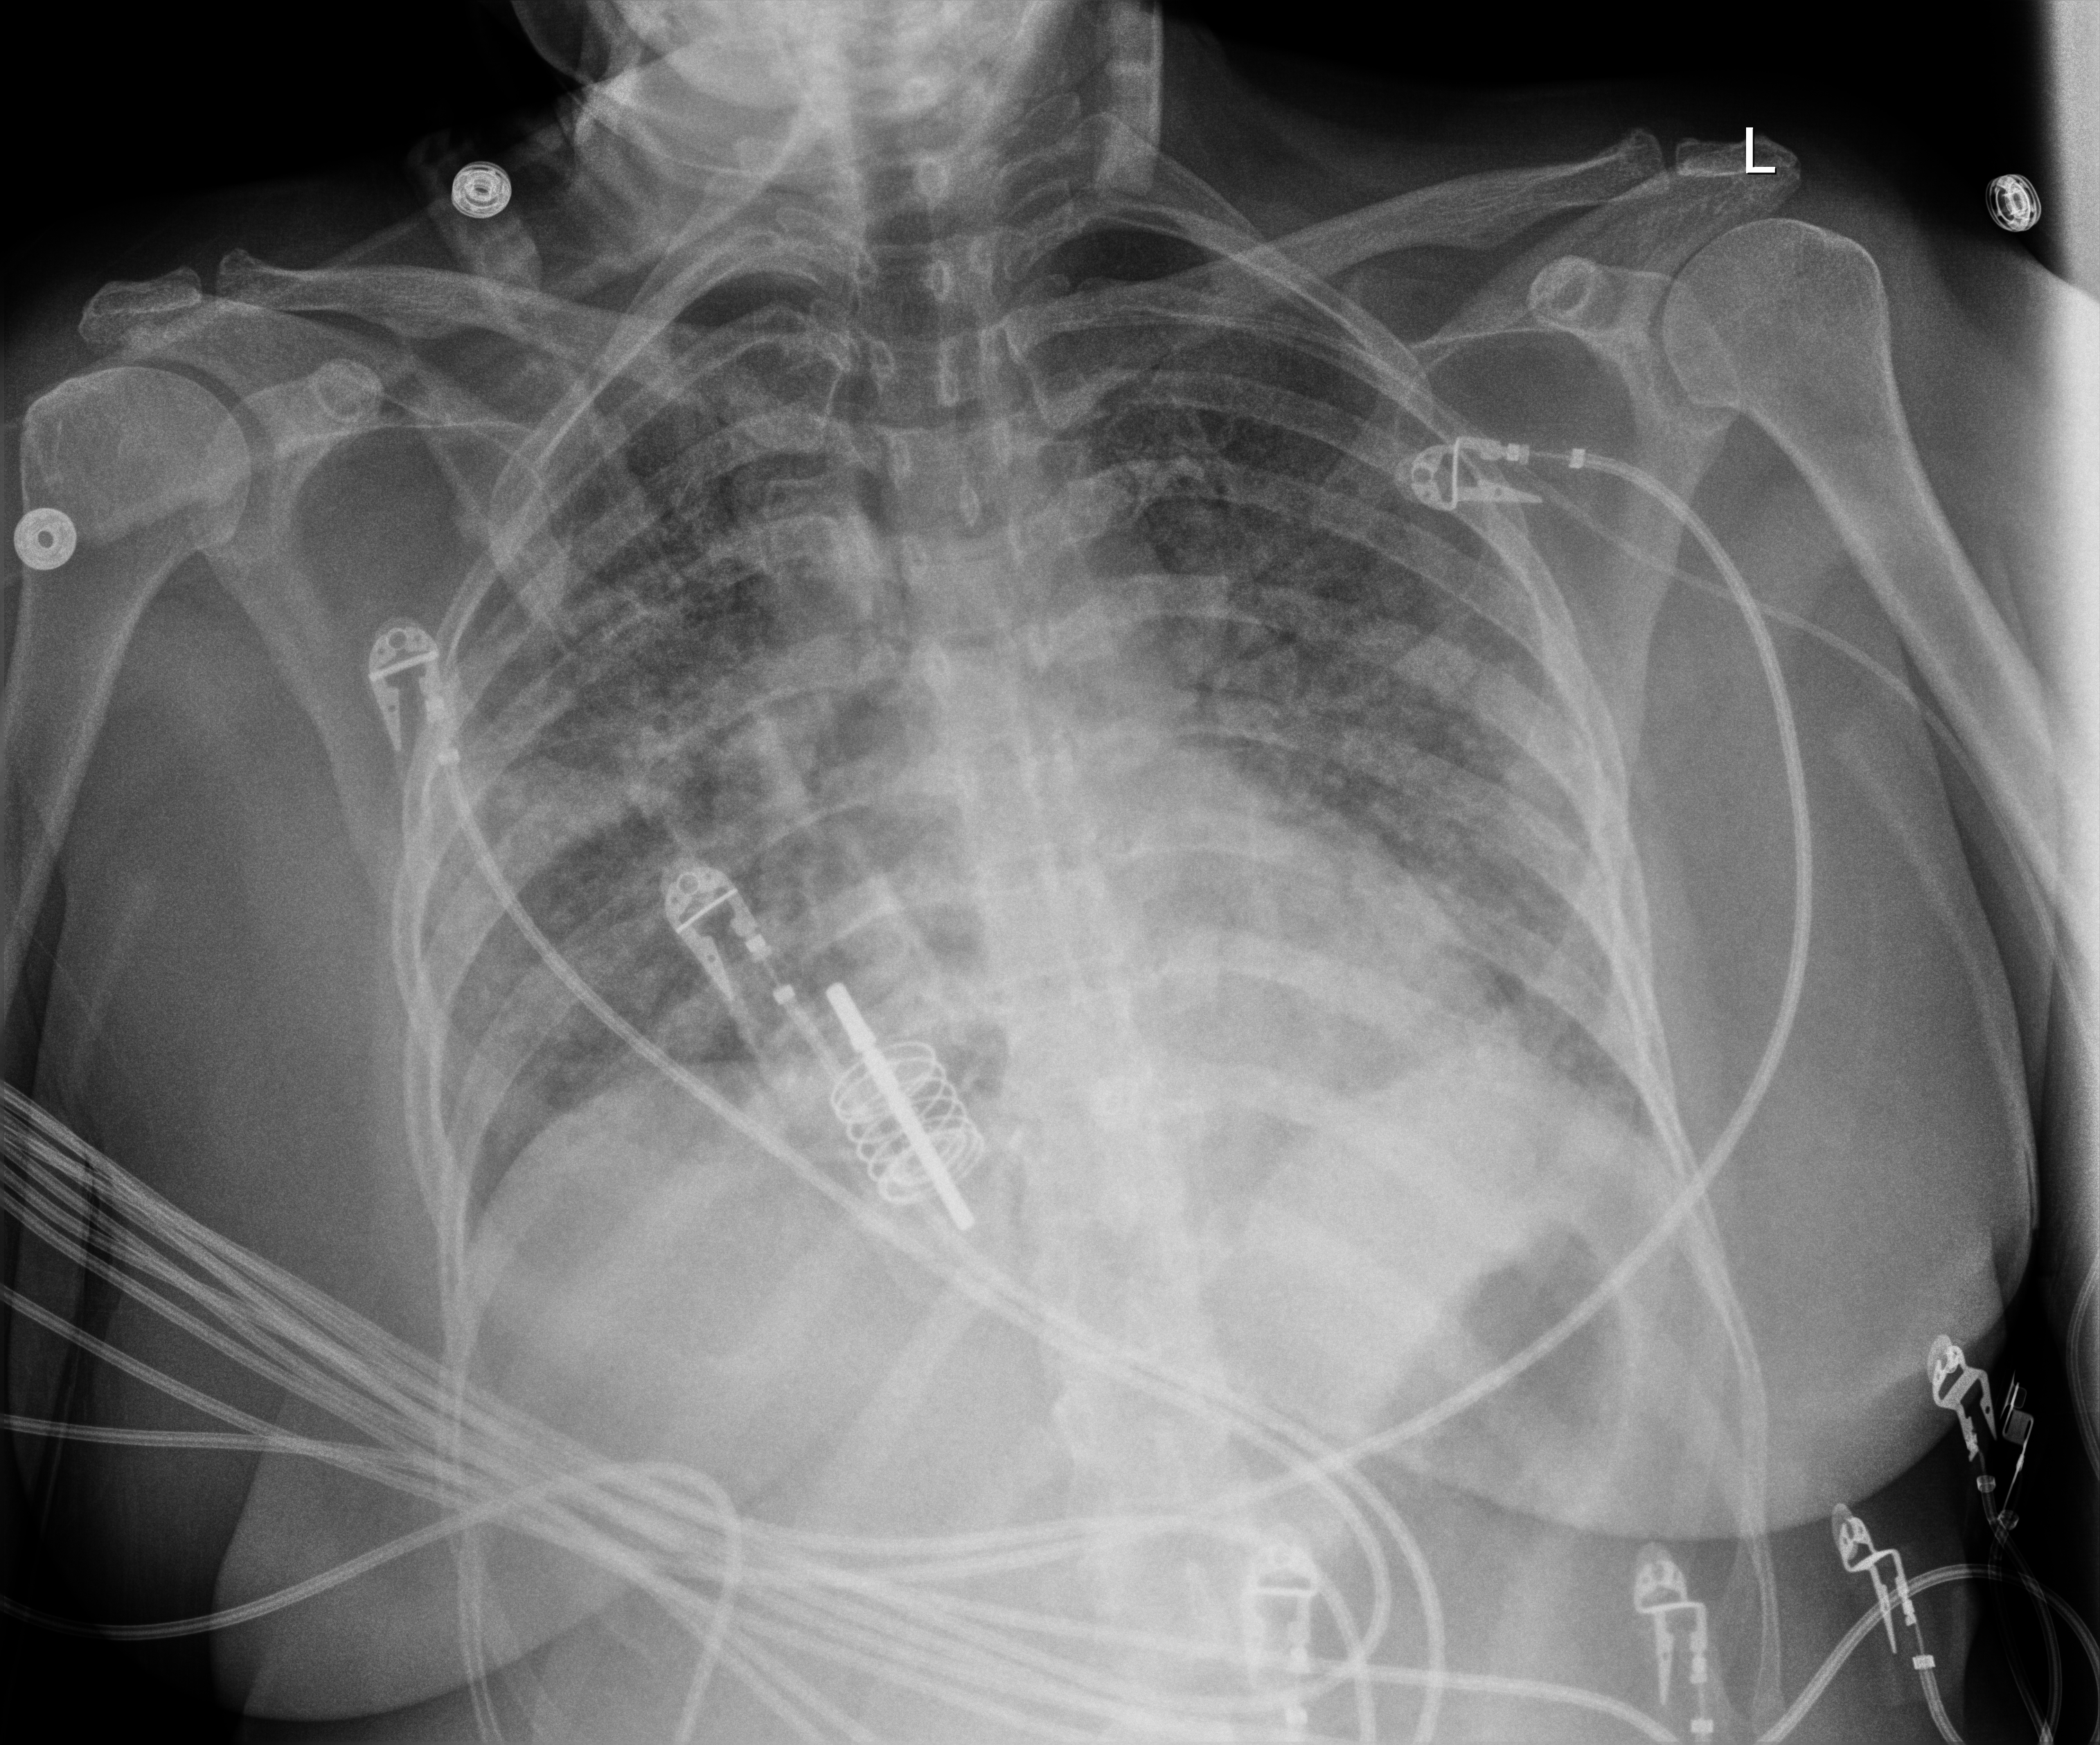
Portable chest radiograph. Patient hospitalised with COVID-19; male, aged 18–59 years.
Admission-level facts for this patient (not findings on this image; timing relative to this image not recorded): length of hospital stay: 38 days.